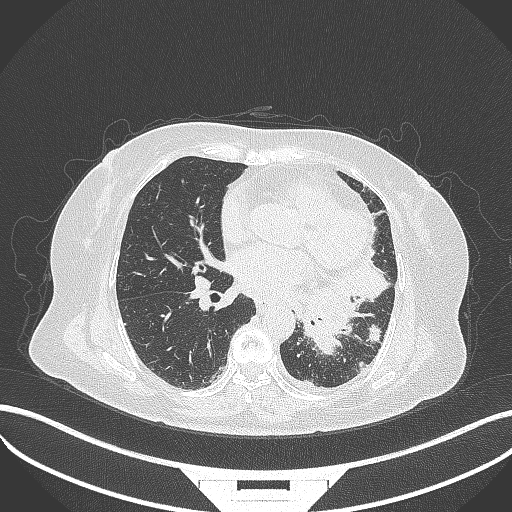
Chest CT, one axial slice. Lung window (W 1500 / L -600 HU). 1 mm slice thickness. 512 × 512 image matrix. Patient: female, 69 years. Case-level facts recorded for this patient, not image findings: clinical TNM (as recorded): T2b N3 M1.
Annotated regions visible in this slice (bounding box drawn by a radiologist):
- lung tumour (recorded histology: adenocarcinoma): box from (x=305, y=253) to (x=390, y=355) px